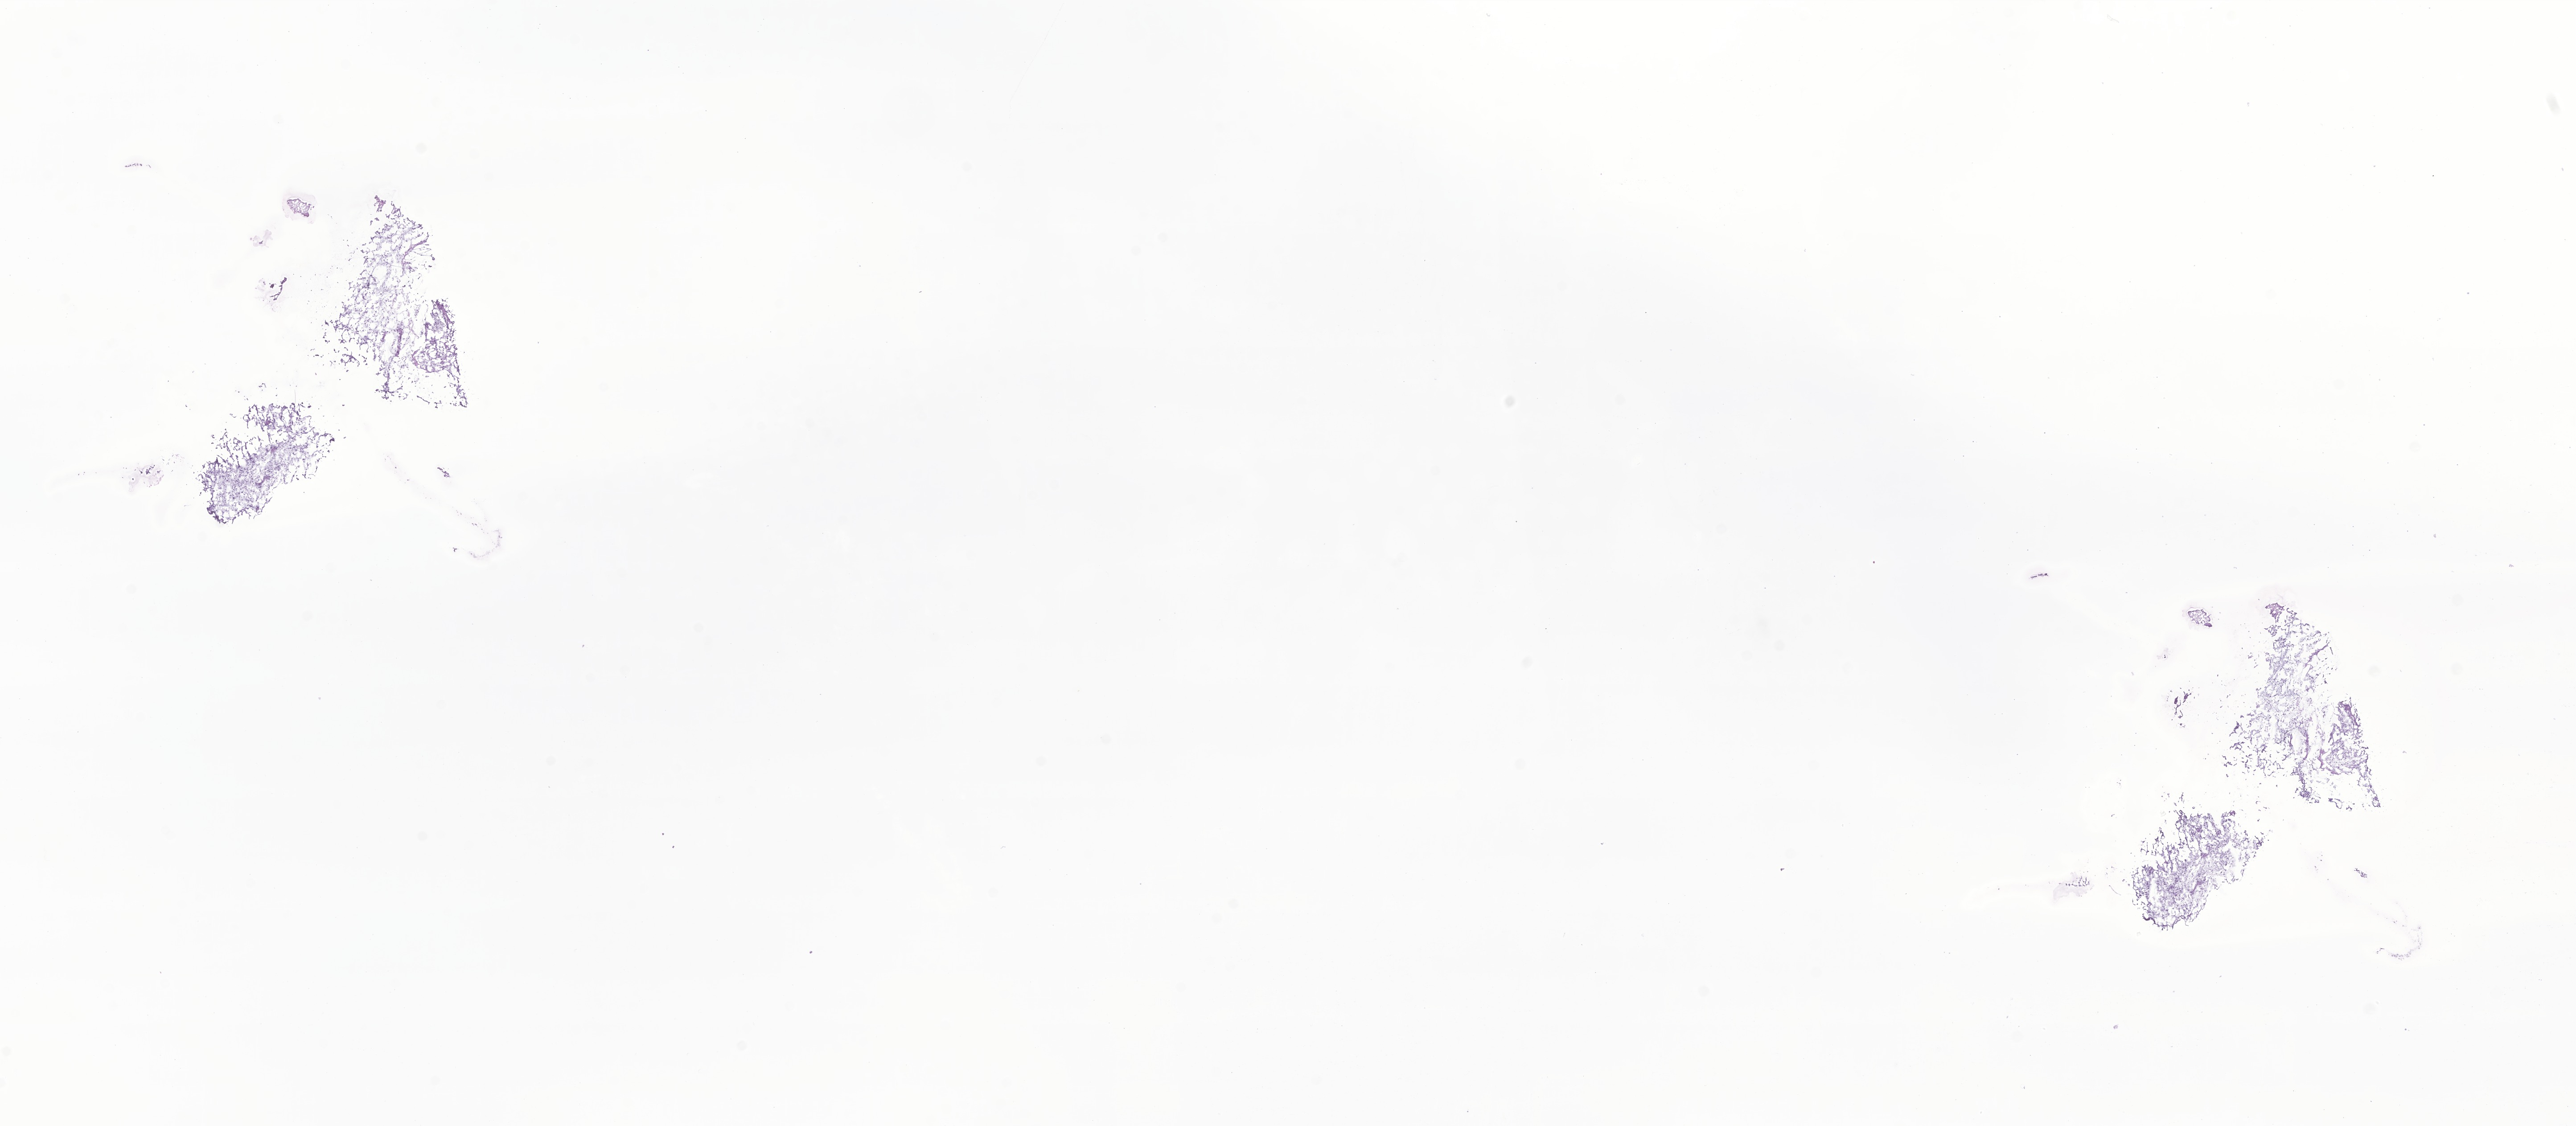
Whole-slide image, H&E stain of tumor tissue from the brain — low-resolution overview of the scanned area, about 24.4 x 10.7 mm. Frozen section (OCT-embedded). Patient male; age 61 months (5 years 1 month).
- recorded diagnosis: Glioma, malignant